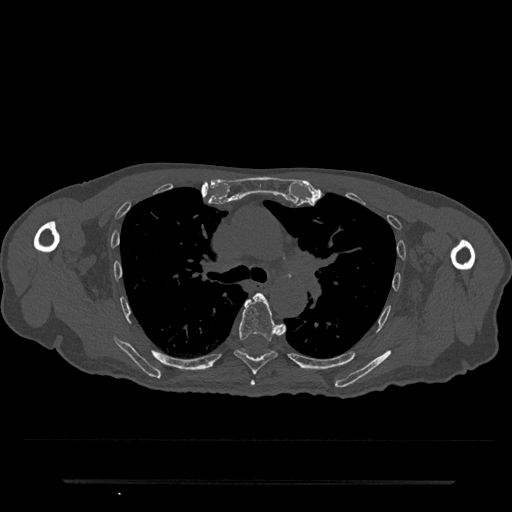
CT including the spine, one axial slice. Position 528 of 797 along the scan axis. 120 kVp. Bone window (W 1800 / L 400 HU). 512 × 512 image matrix. Male patient, age 74 years. From the clinical record (not read from this slice): primary cancer: prostate.
Outlined on this slice (semi-automatically segmented with operator editing):
- T5 vertebra: bounding box [x1, y1, x2, y2] px = [250, 380, 255, 386]
- T6 vertebra: [234, 293, 285, 375]